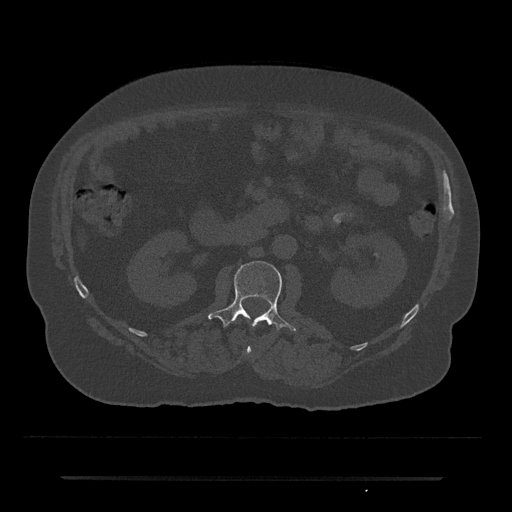
CT including the spine, one axial slice; reconstruction kernel Br40s/3; 120 kVp; bone window (W 1800 / L 400 HU); 512 × 512 image matrix, field of view 437 × 437 mm. Male patient, age 69 years. Case-level facts recorded for this patient, not image findings: primary cancer: prostate.
Outlined on this slice (semi-automatically segmented with operator editing):
- L1 vertebra: bounding box (x1, y1, x2, y2) in pixels: (236, 317, 252, 354)
- L2 vertebra: (208, 261, 296, 331)